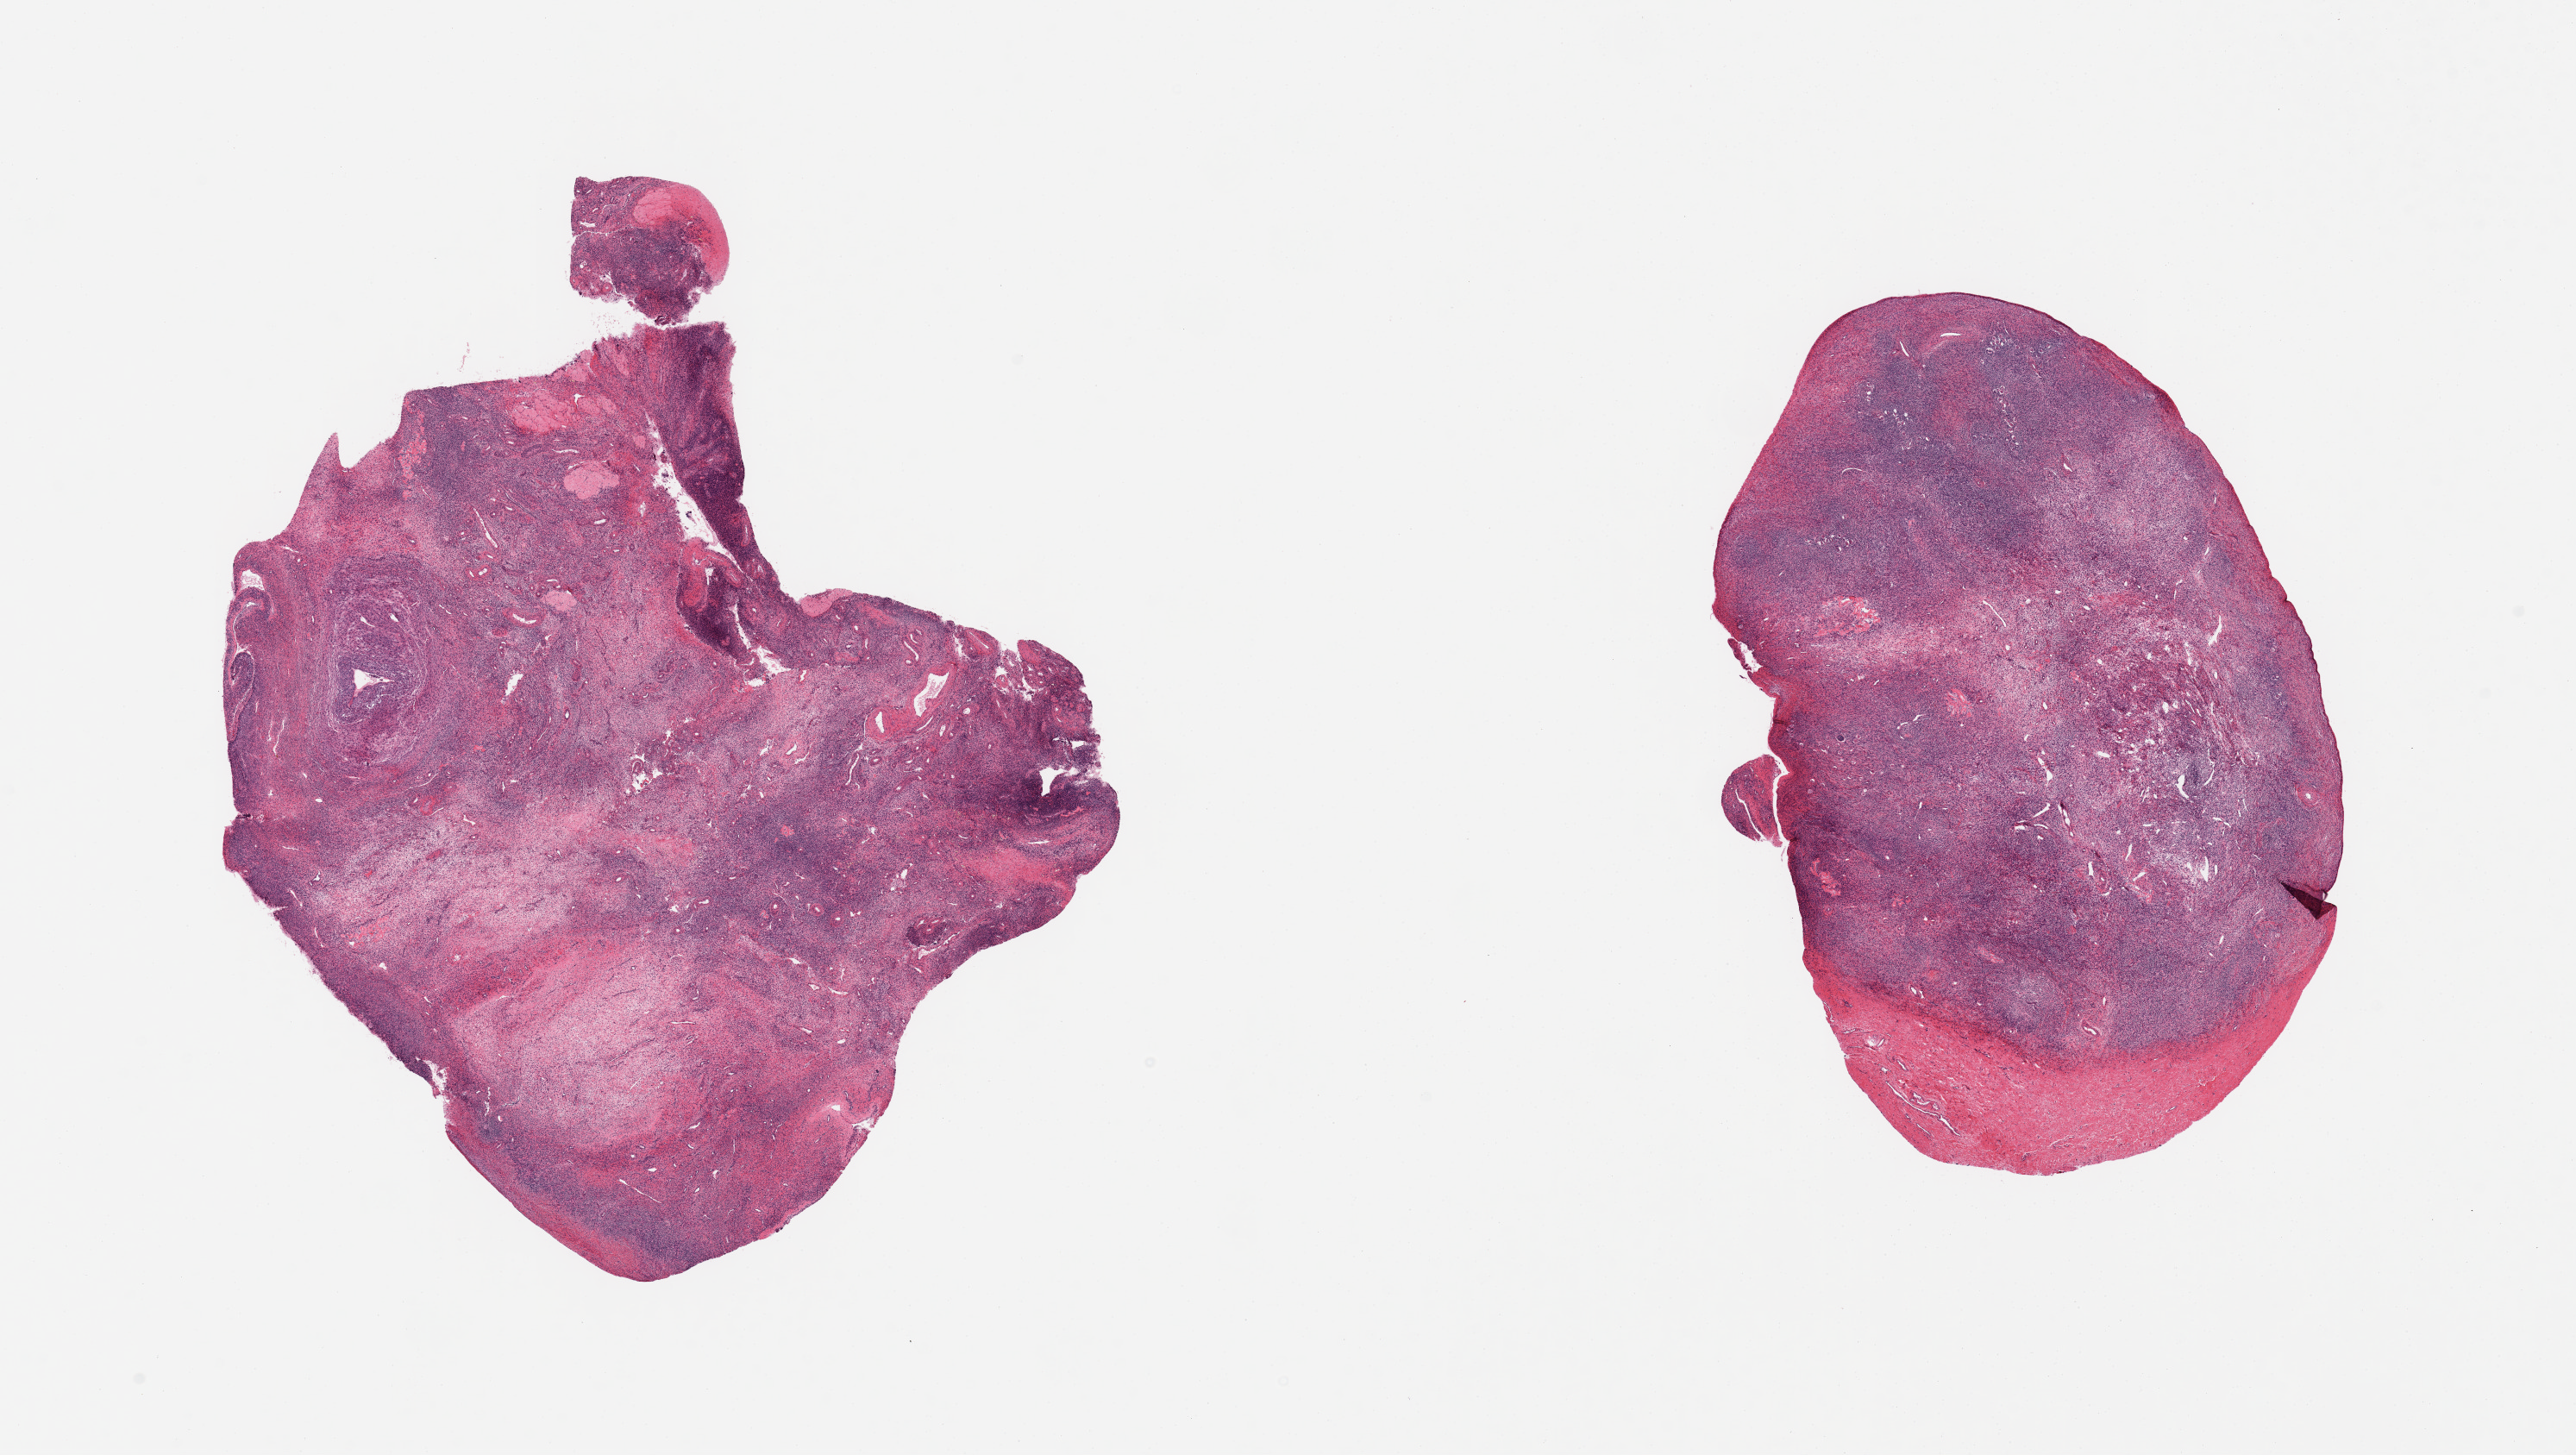
Hematoxylin and eosin (H&E) whole-slide image — whole scanned area (about 23.6 x 13.3 mm) shown as a low-resolution overview, PAXgene-fixed paraffin-embedded (PFPE) section, sampled site (target tissue): ovary, tissue donor sample.
Pathologist's review note for this sample: 2 ; numerous ova and corpora; 1 mm thick fibrous 'cap' at end of 1 piece.